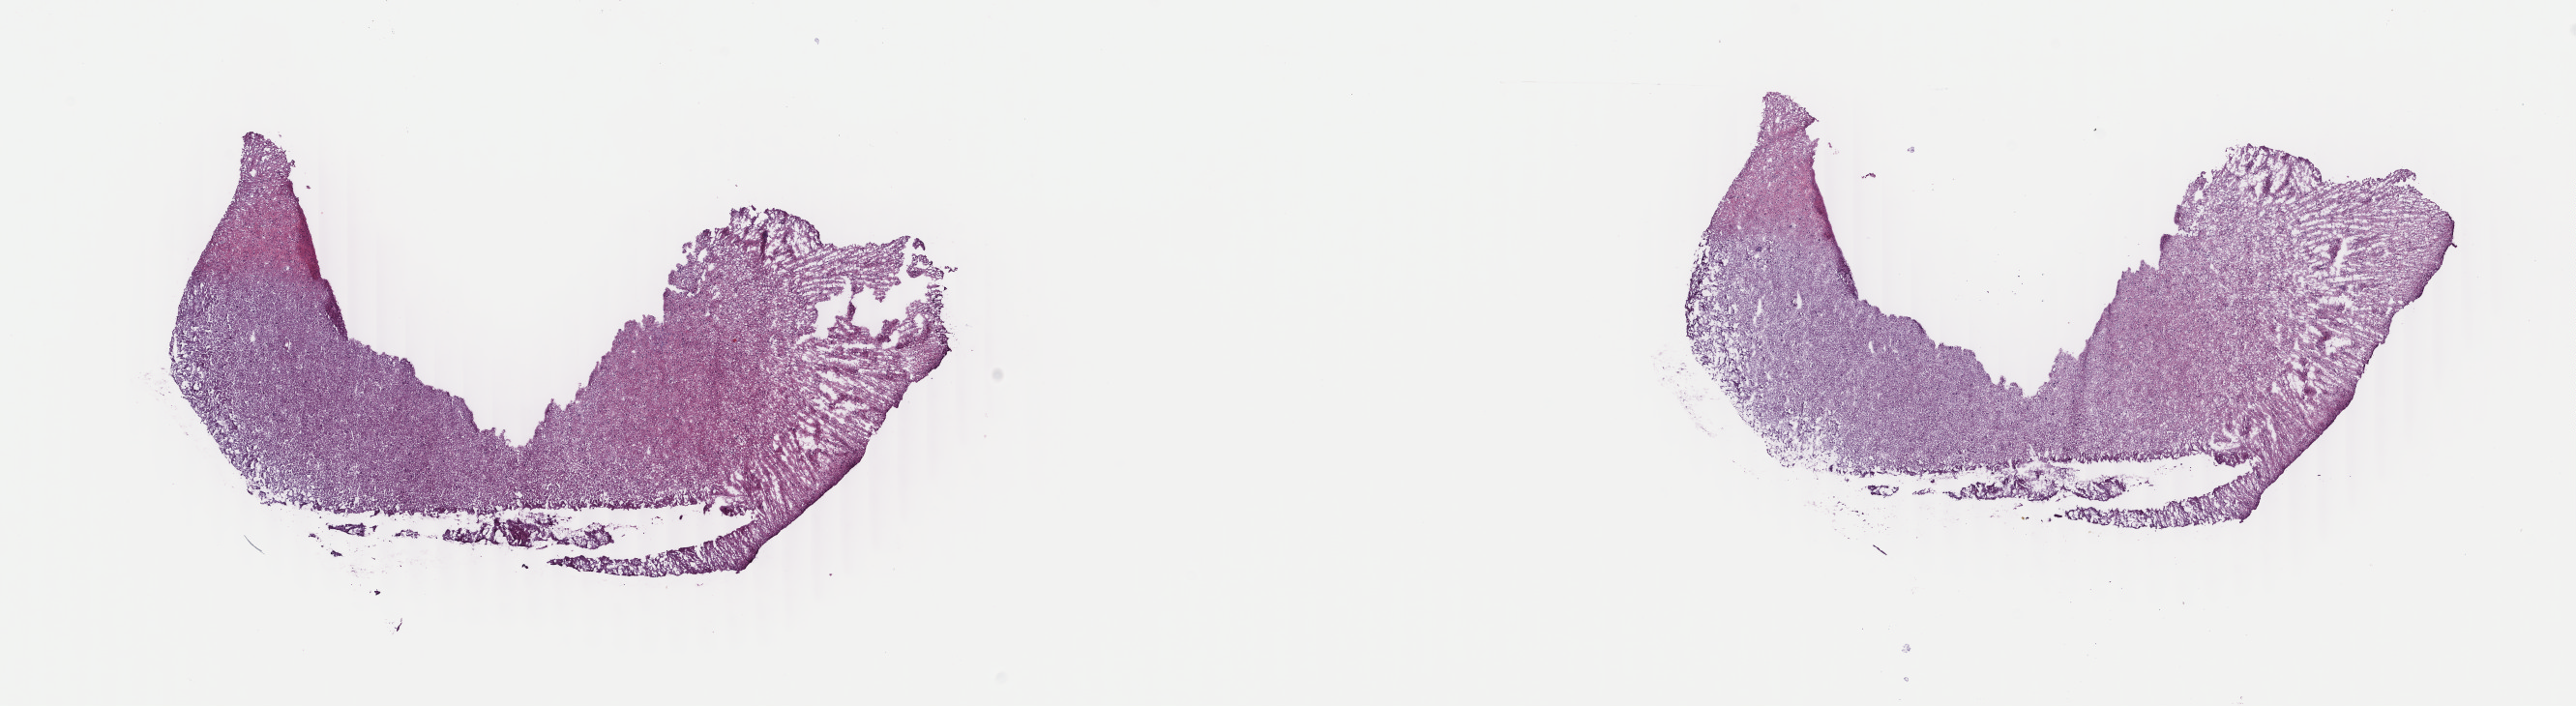
Digitized H&E tissue section (whole slide) — whole scanned area (about 21.2 x 5.8 mm, from a 40x scan) shown as a low-resolution overview. Frozen section. Primary tumour sample from the brain. Patient: female, age at initial diagnosis 56 years. Histologic grade: G2 (moderately differentiated). Slide review estimates, as recorded: tumour cells 40%, tumour nuclei 70%, normal cells 10%, stromal cells 50%, necrosis 0%. Infiltration values recorded for this section: lymphocyte infiltration 0%, monocyte infiltration 0%, neutrophil infiltration 0%.
- histologic diagnosis: Mixed glioma (cerebrum)